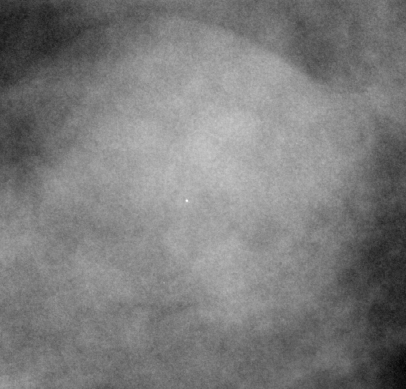
Region of interest cut from a scanned film mammogram (one marked finding); right breast; MLO view; BI-RADS breast density category 3 (scale 1–4).
Mass, shape oval, margins obscured; BI-RADS assessment category 3; subtlety rating 5 on a 1 (subtle) to 5 (obvious) scale; pathology (as recorded): benign.